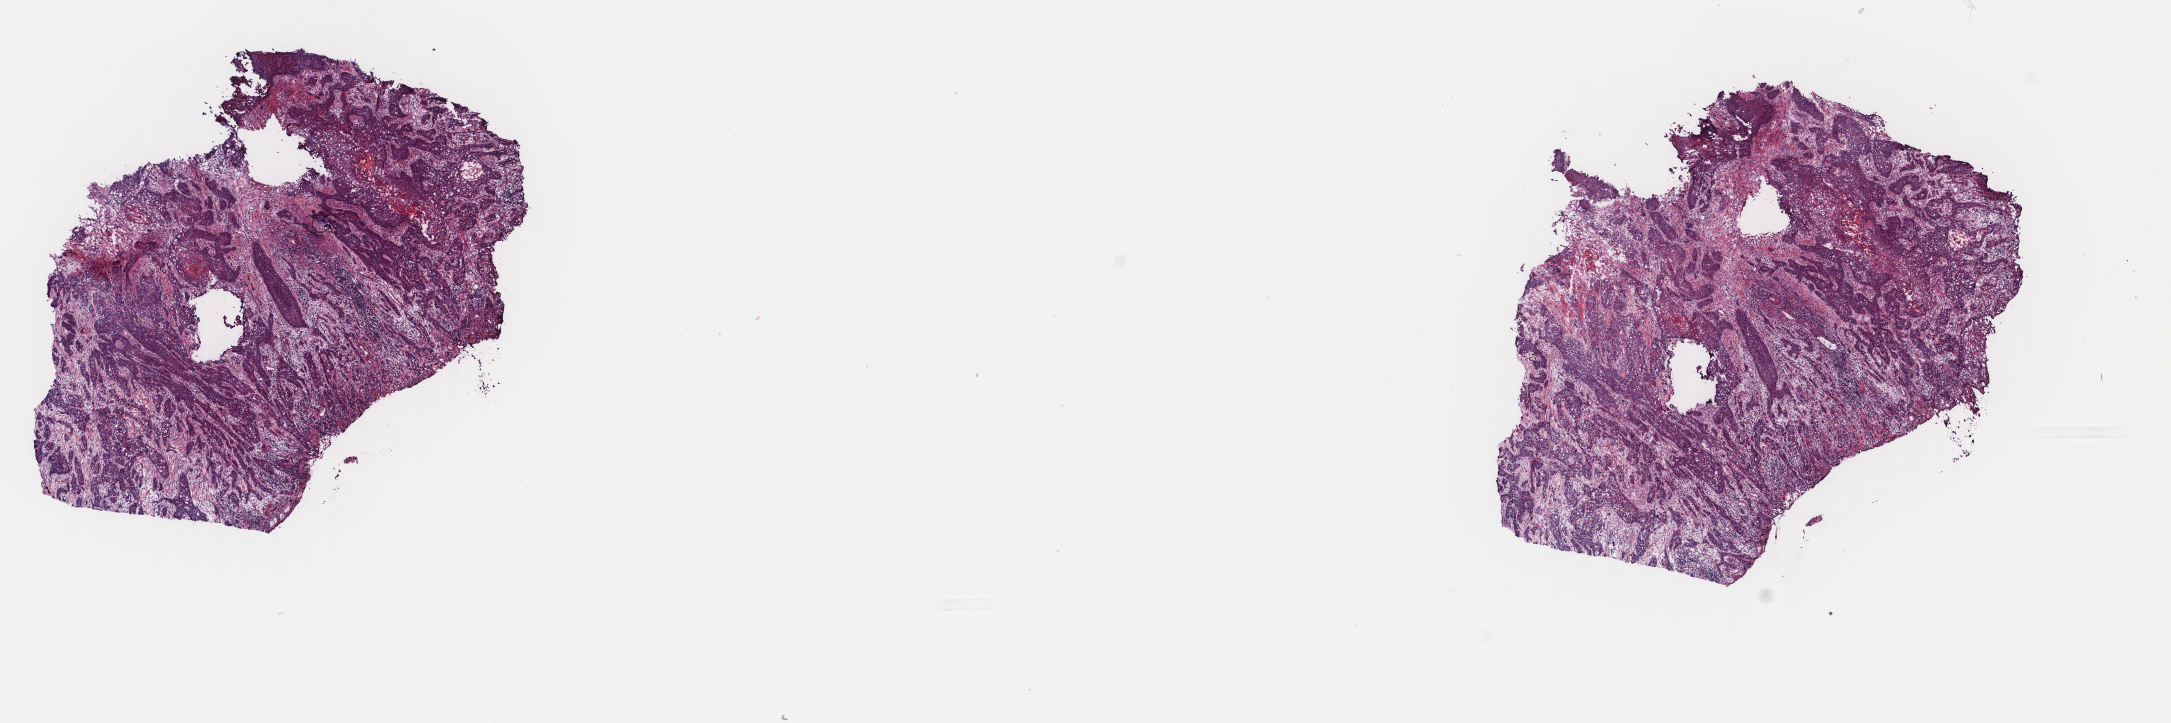
Digitized Hematoxylin and eosin (H&E) stained tissue section (whole slide), shown as a low-resolution overview of the whole scanned area (about 17.2 x 5.7 mm), frozen section from the top of the tissue portion, primary tumour sample from the head and neck. Patient: male, age at initial diagnosis 67 years.
Pathologic diagnosis: Squamous cell carcinoma, NOS (tonsil, NOS).